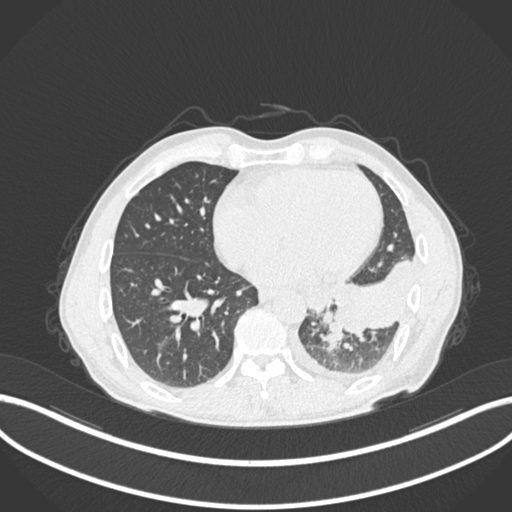
Chest CT, one axial slice. Slice 85 of 222 in the series (ordered by position). 120 kVp. Lung window (W 1500 / L -600 HU). 1 mm slice thickness. 512 × 512 image matrix. Patient: male, 47 years. From the clinical record (not read from this slice): clinical TNM (as recorded): T3 N1 M1c; histopathological grade: G3.
Structures marked on this image (bounding box drawn by a radiologist):
- lung tumour (recorded histology: small cell carcinoma): bounding box [x1, y1, x2, y2] px = [318, 317, 349, 352]